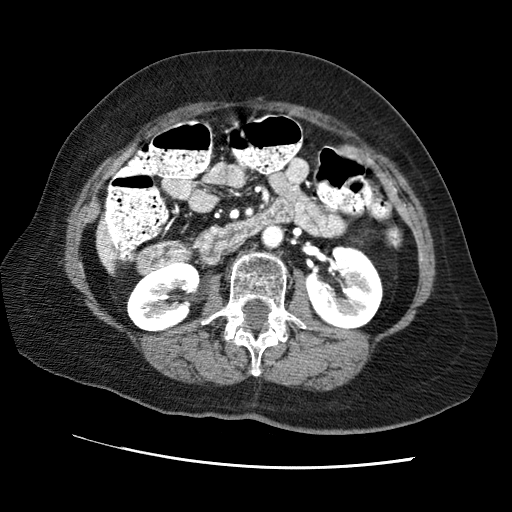
Contrast-enhanced abdominal CT (liver protocol), one axial slice. Position 12 of 65 along the scan axis. Soft-tissue window (W 400 / L 40 HU). 512 × 512 image matrix, field of view 340 × 340 mm. Case-level facts recorded for this patient, not image findings: diagnosis: hepatocellular carcinoma (patient treated with transarterial chemoembolisation; whether this scan precedes or follows treatment is not stated here); TNM stage (as recorded): Stage-II; Child-Pugh class: A; tumour differentiation: no biopsy; tumour nodularity: multinodular.
Outlined on this slice (semi-automatic segmentation, software-assisted and operator-edited):
- liver parenchyma outside the tumour (the mass and vessels are separate outlines, so this box may not span the whole liver): box from (x=96, y=224) to (x=116, y=272) px
- liver vessels: (x=106, y=250)–(x=112, y=257)